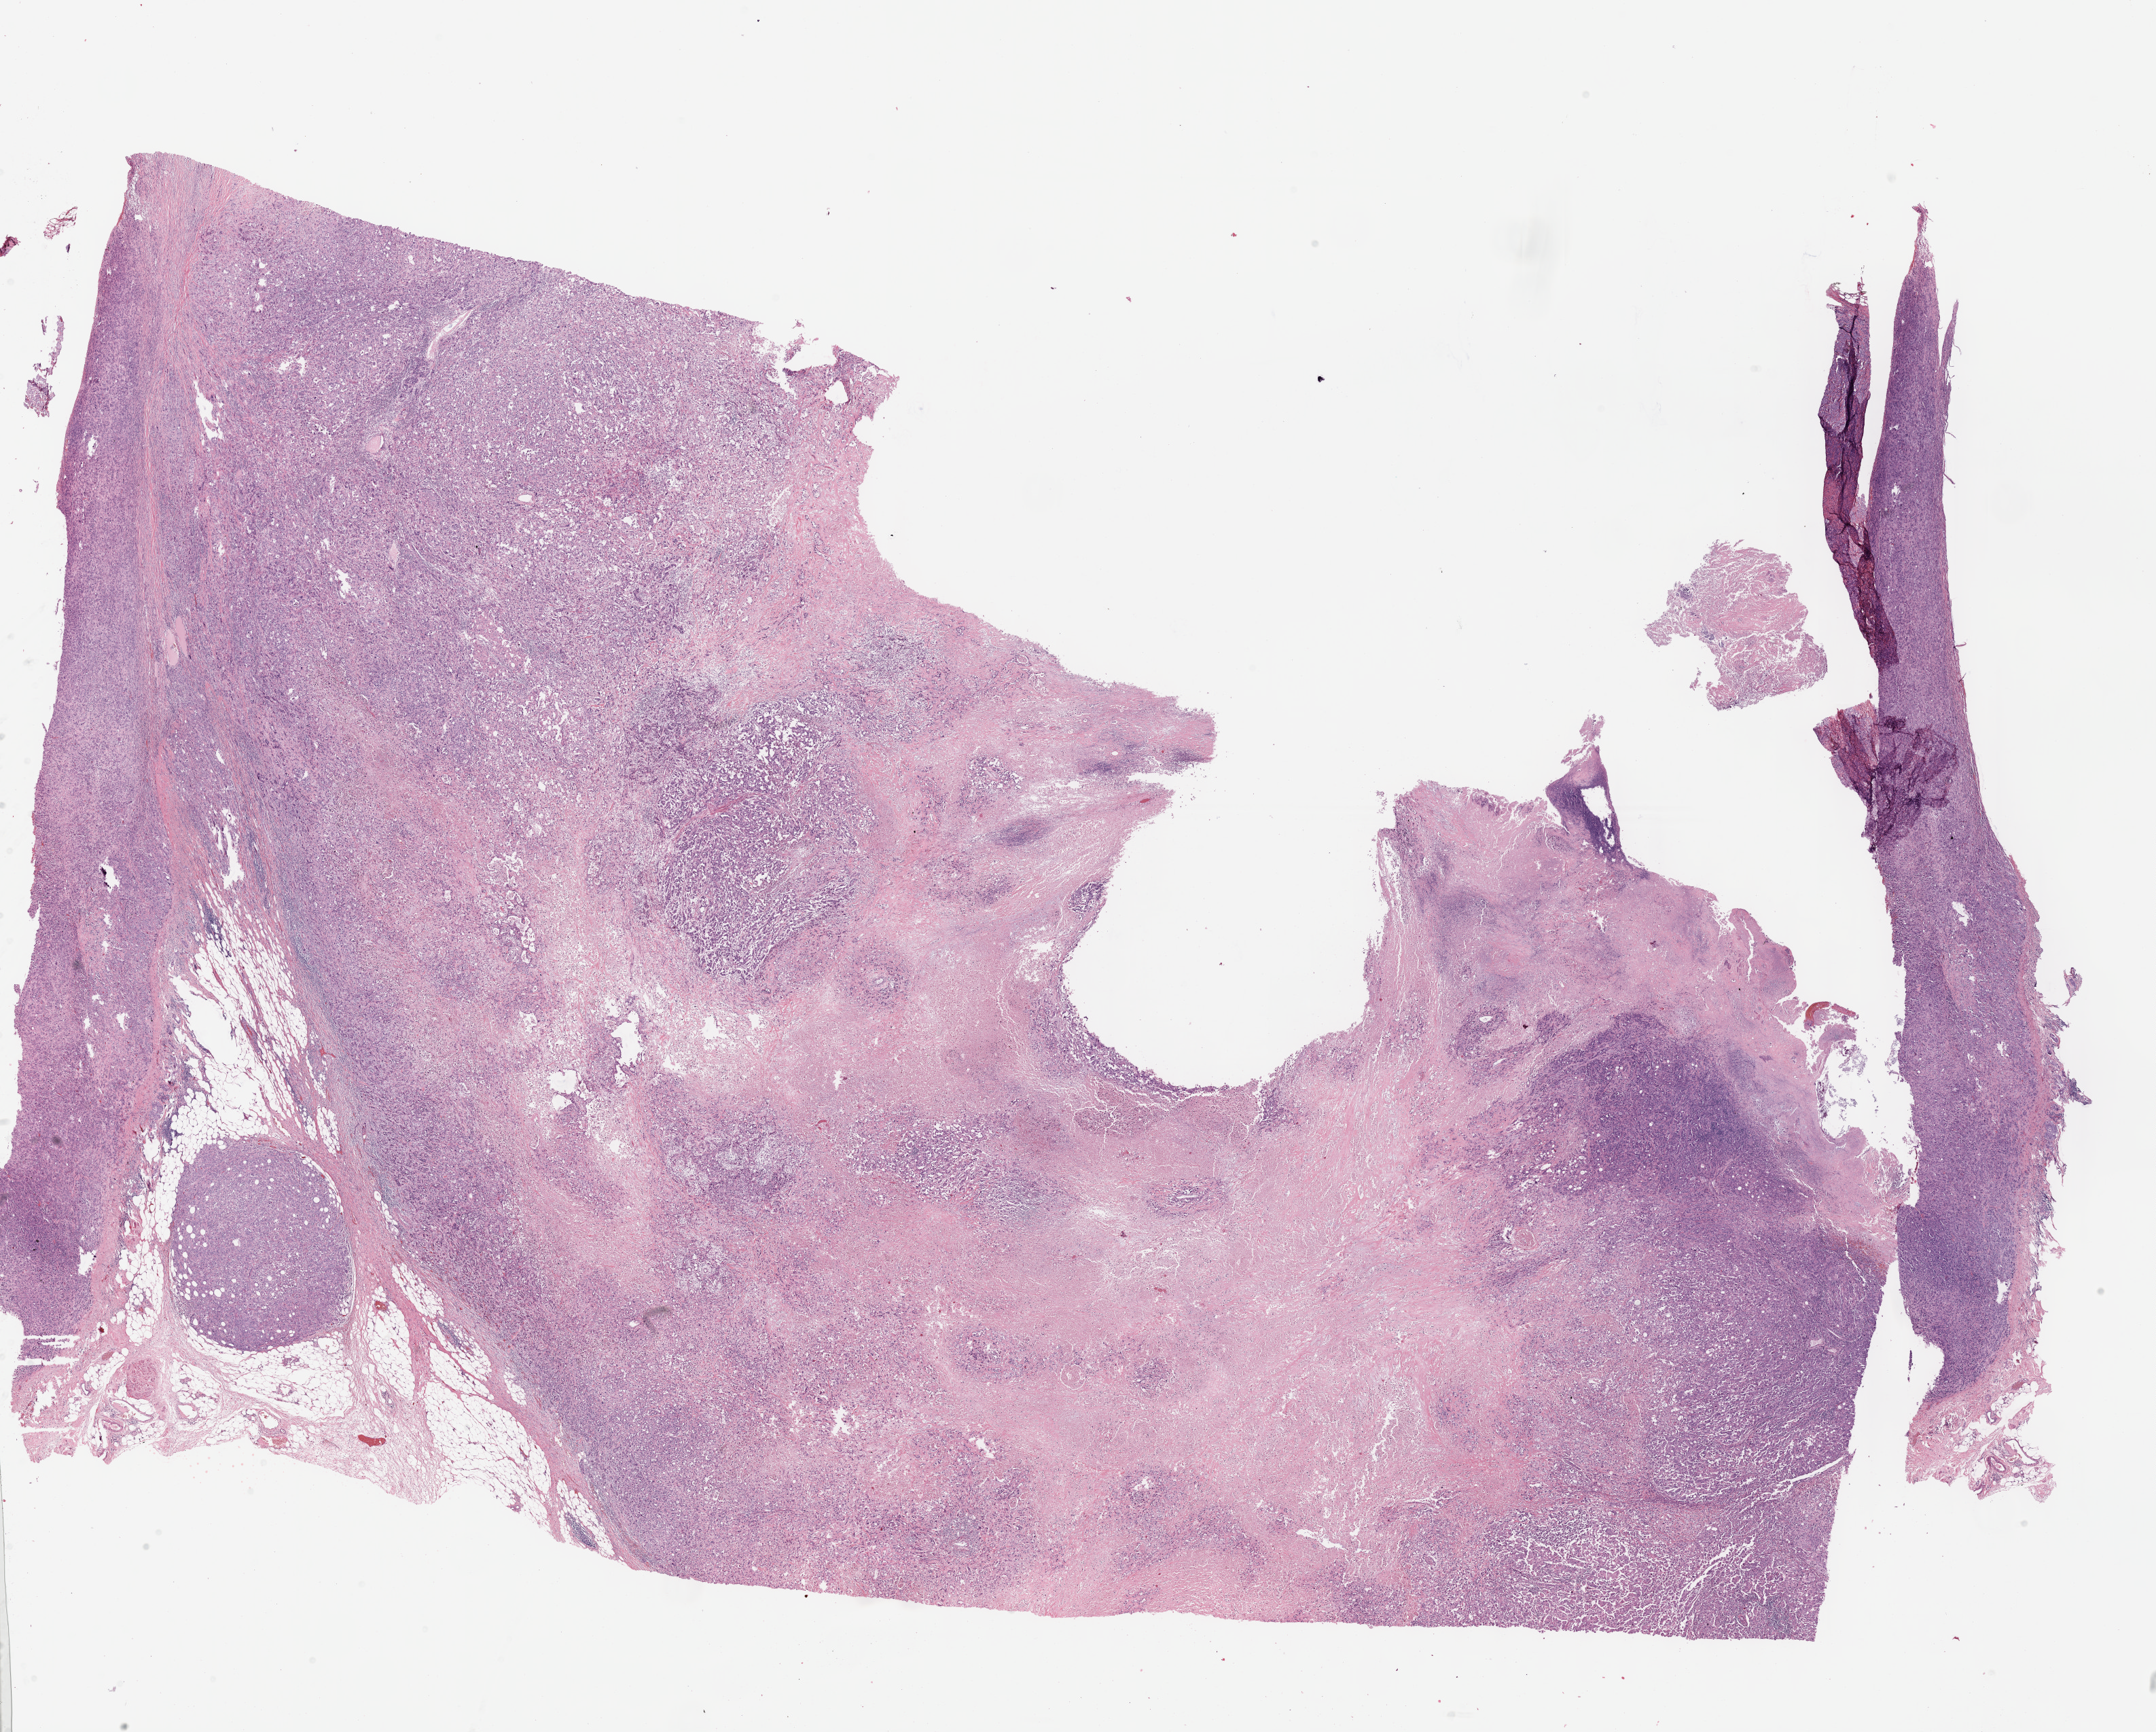
Digitized Hematoxylin and eosin (H&E) stained tissue section (whole slide) — whole scanned area (about 25.7 x 20.6 mm, acquisition: 40x scan) shown as a low-resolution overview, formalin-fixed paraffin-embedded (FFPE) diagnostic section, primary tumour sample from the bladder. Patient: male, age at initial diagnosis 61 years. Histologic grade: high grade.
Lymph nodes positive (case pathology): 2 of 2 examined. AJCC pathologic stage: IV (7th edition). Pathologic diagnosis: Transitional cell carcinoma.